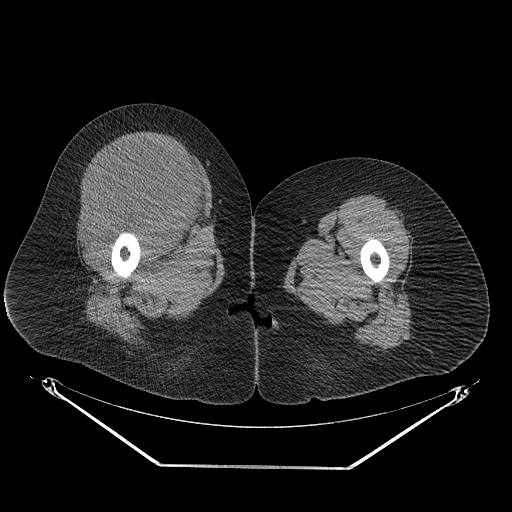
CT of an extremity soft-tissue mass (from a PET/CT study), one axial slice. Position 42 of 267 along the scan axis. Soft-tissue window (W 400 / L 40 HU). 512 × 512 image matrix. Female patient. From the clinical record (not read from this slice): histological type: malignant solitary fibrous tumor; grade: intermediate; site of the primary tumour: right thigh.
Outlined on this slice (expert contour drawn on MRI and transferred to this co-registered scan by the dataset authors):
- gross tumour volume including surrounding oedema: bounding box (x1, y1, x2, y2) in pixels: (78, 139, 209, 236)
- gross tumour volume (mass): (85, 139, 204, 234)